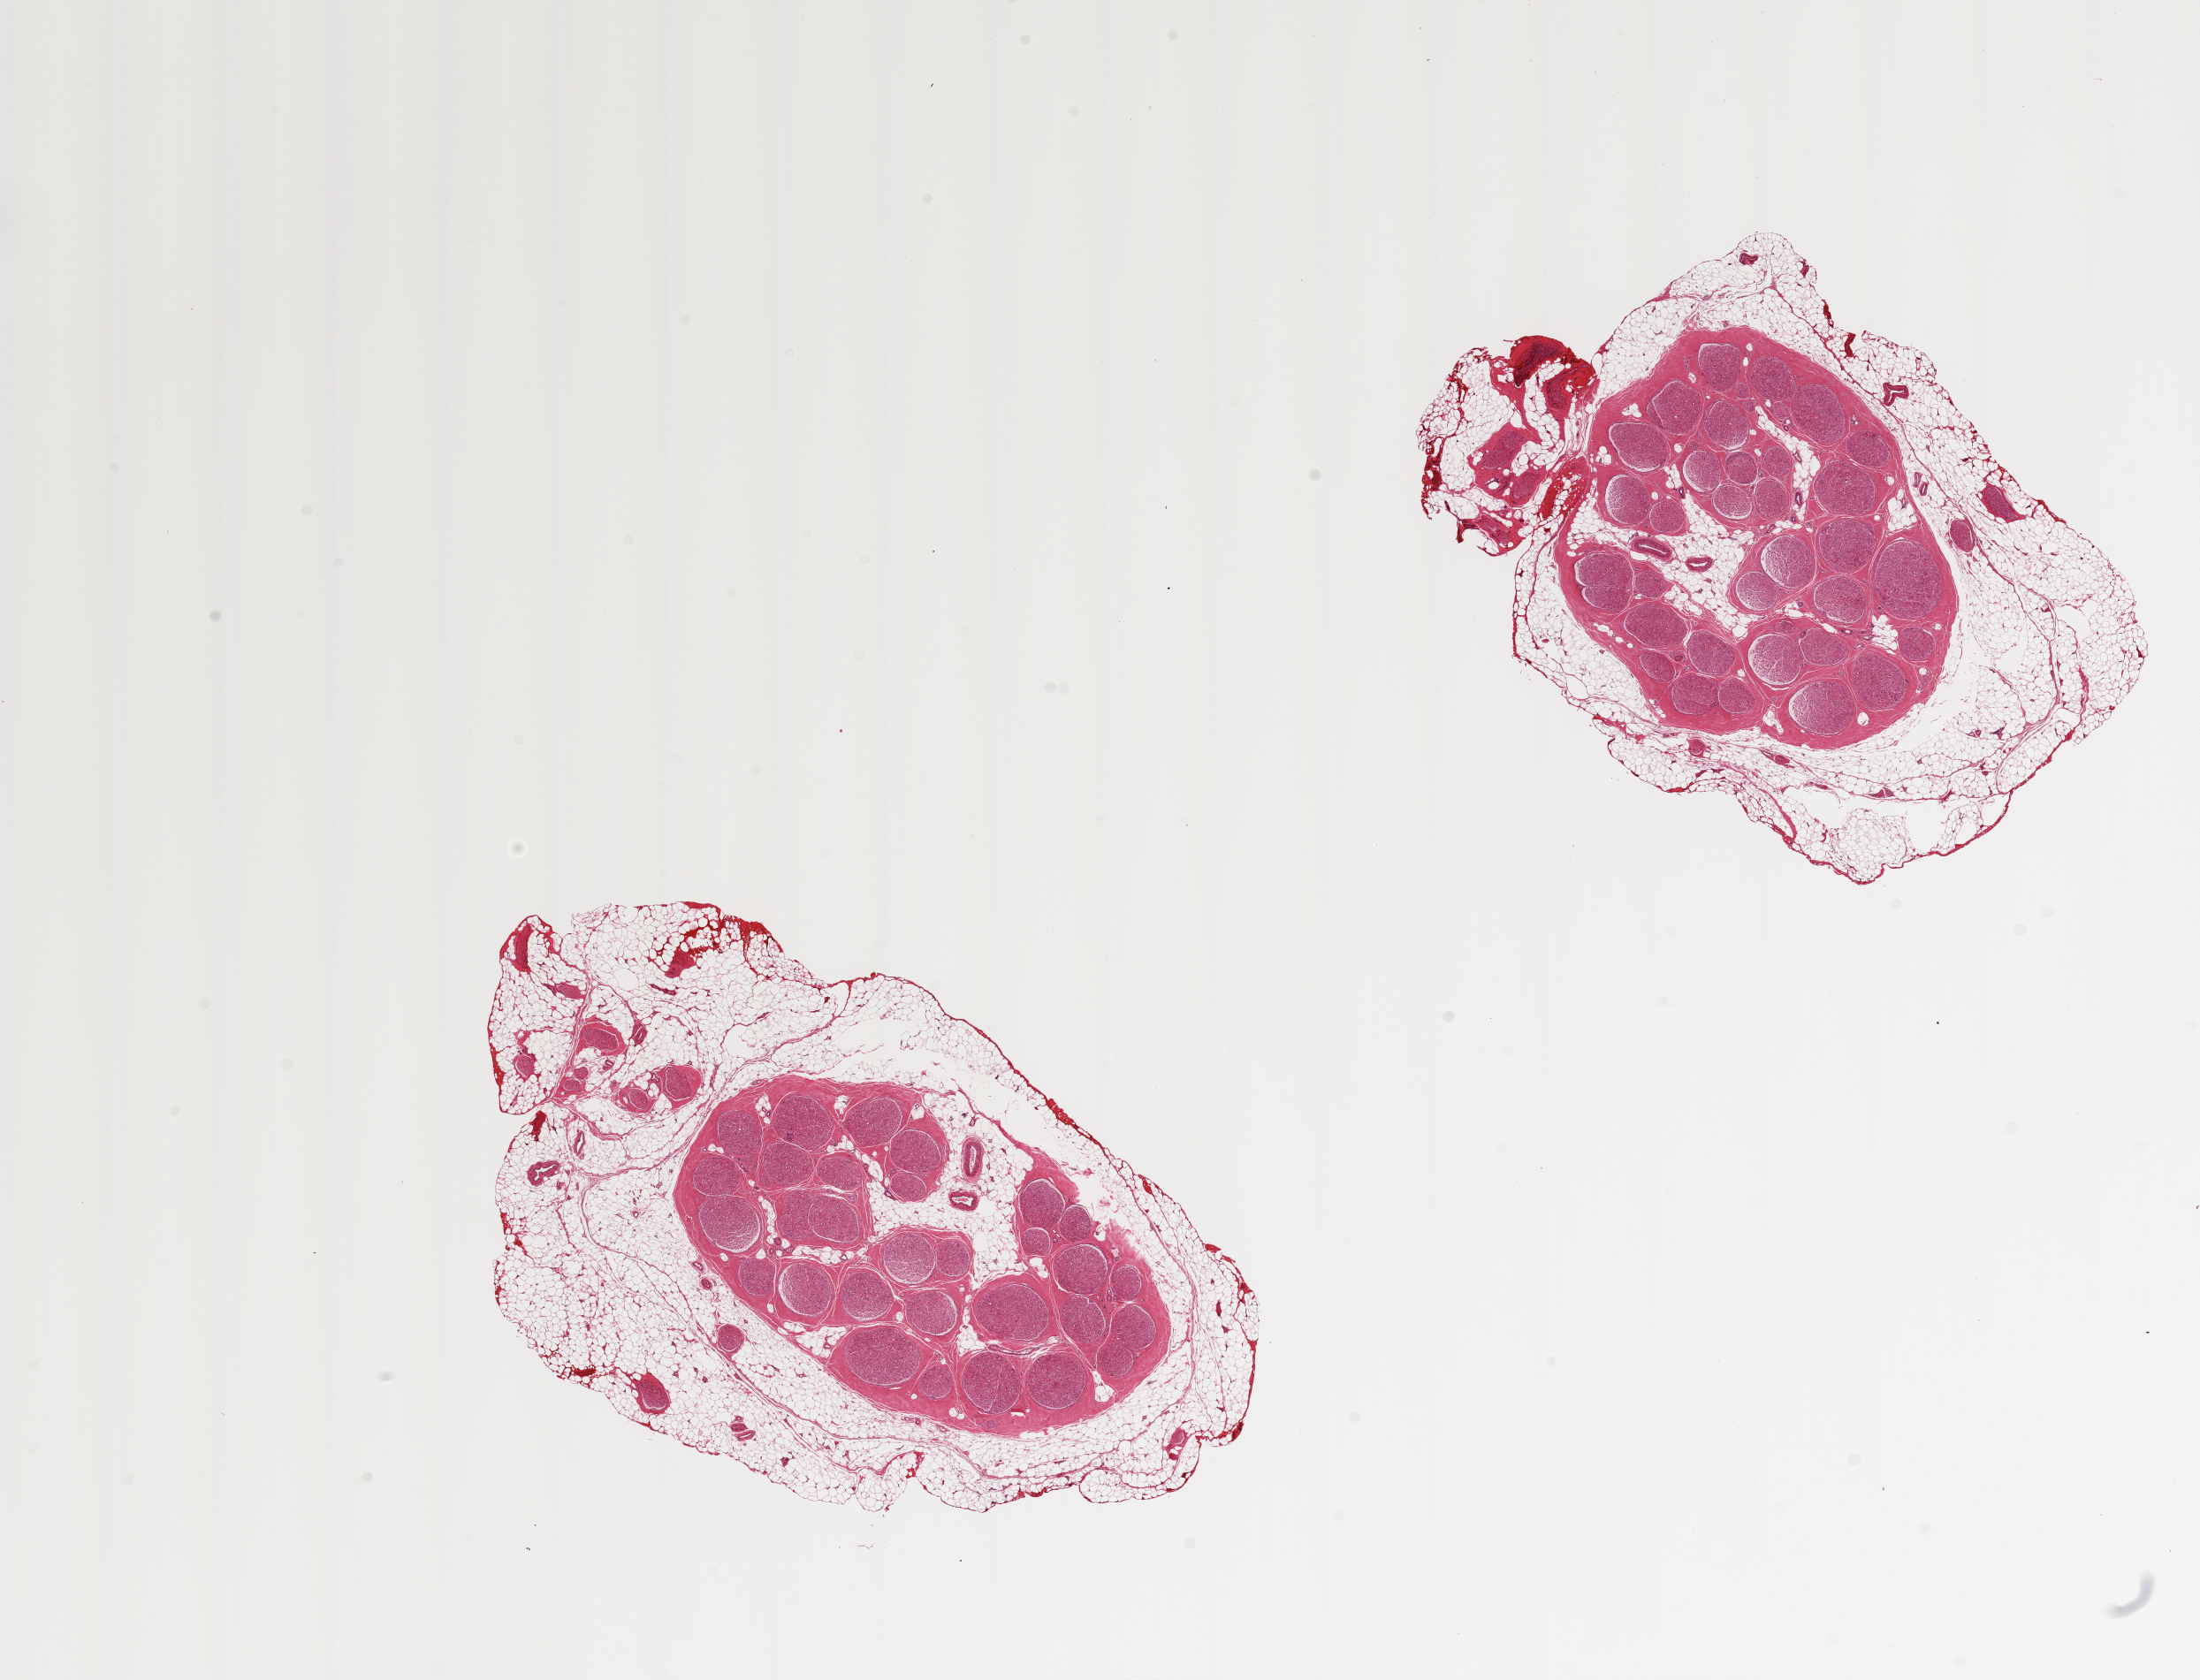
Whole-slide image, haematoxylin and eosin stain, a low-resolution overview of the entire scanned area, about 19.7 x 15.0 mm; PAXgene-fixed paraffin-embedded (PFPE) section; target tissue: tibial nerve; tissue donor sample.
Review note (as recorded): 2 pieces rims of adherent fat up to ~2mm.